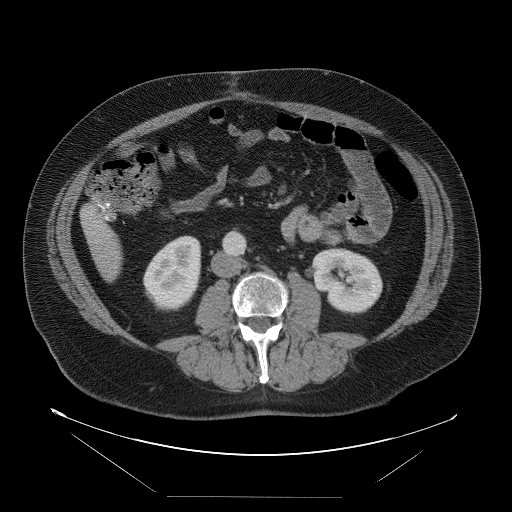
Contrast-enhanced abdominal CT, one axial slice. Slice 17 of 114 in the series (ordered by position). Soft-tissue window (W 400 / L 40 HU). 512 × 512 image matrix. Male patient, age 61 years. From the clinical record (not read from this slice): diagnosis: colorectal cancer liver metastases, imaged before liver resection; multiple liver metastases: no; largest metastasis: 6.5 cm; chemotherapy before resection: no.
Outlined on this slice (manually delineated by an expert):
- liver: bounding box [x1, y1, x2, y2] px = [82, 206, 123, 280]